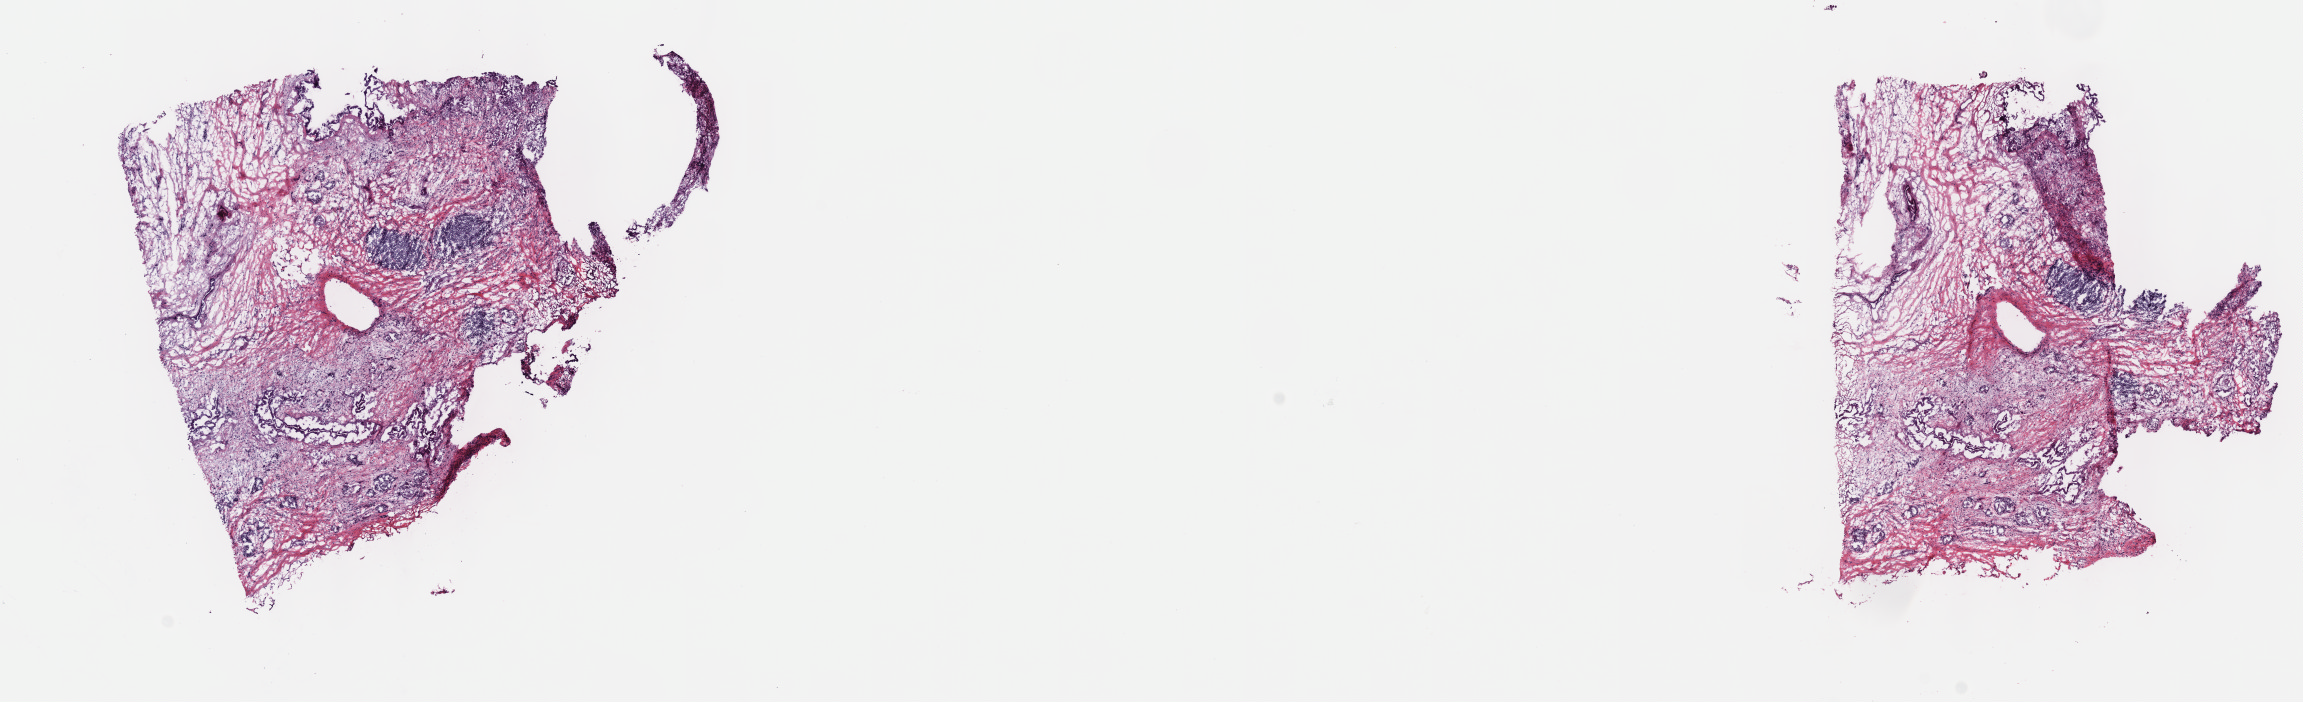
Digitized H&E tissue section (whole slide), whole scanned area (about 18.6 x 5.7 mm, from a 40x scan) shown as a low-resolution overview. Frozen section from the top of the tissue portion. Sample: primary tumour, pancreas. Female patient; age at initial diagnosis 80 years. Histologic grade: G2 (moderately differentiated). Composition of this section per pathologist review: tumour cells 20%, tumour nuclei 25%, normal cells 50%, stromal cells 30%, necrosis 0%. Inflammatory infiltration, as recorded: lymphocyte infiltration 10%, monocyte infiltration 2%, neutrophil infiltration 0%.
Lymph nodes positive (case pathology): 8 of 24 examined. AJCC pathologic stage: IIB. Pathologic diagnosis: Adenocarcinoma with mixed subtypes (head of pancreas).